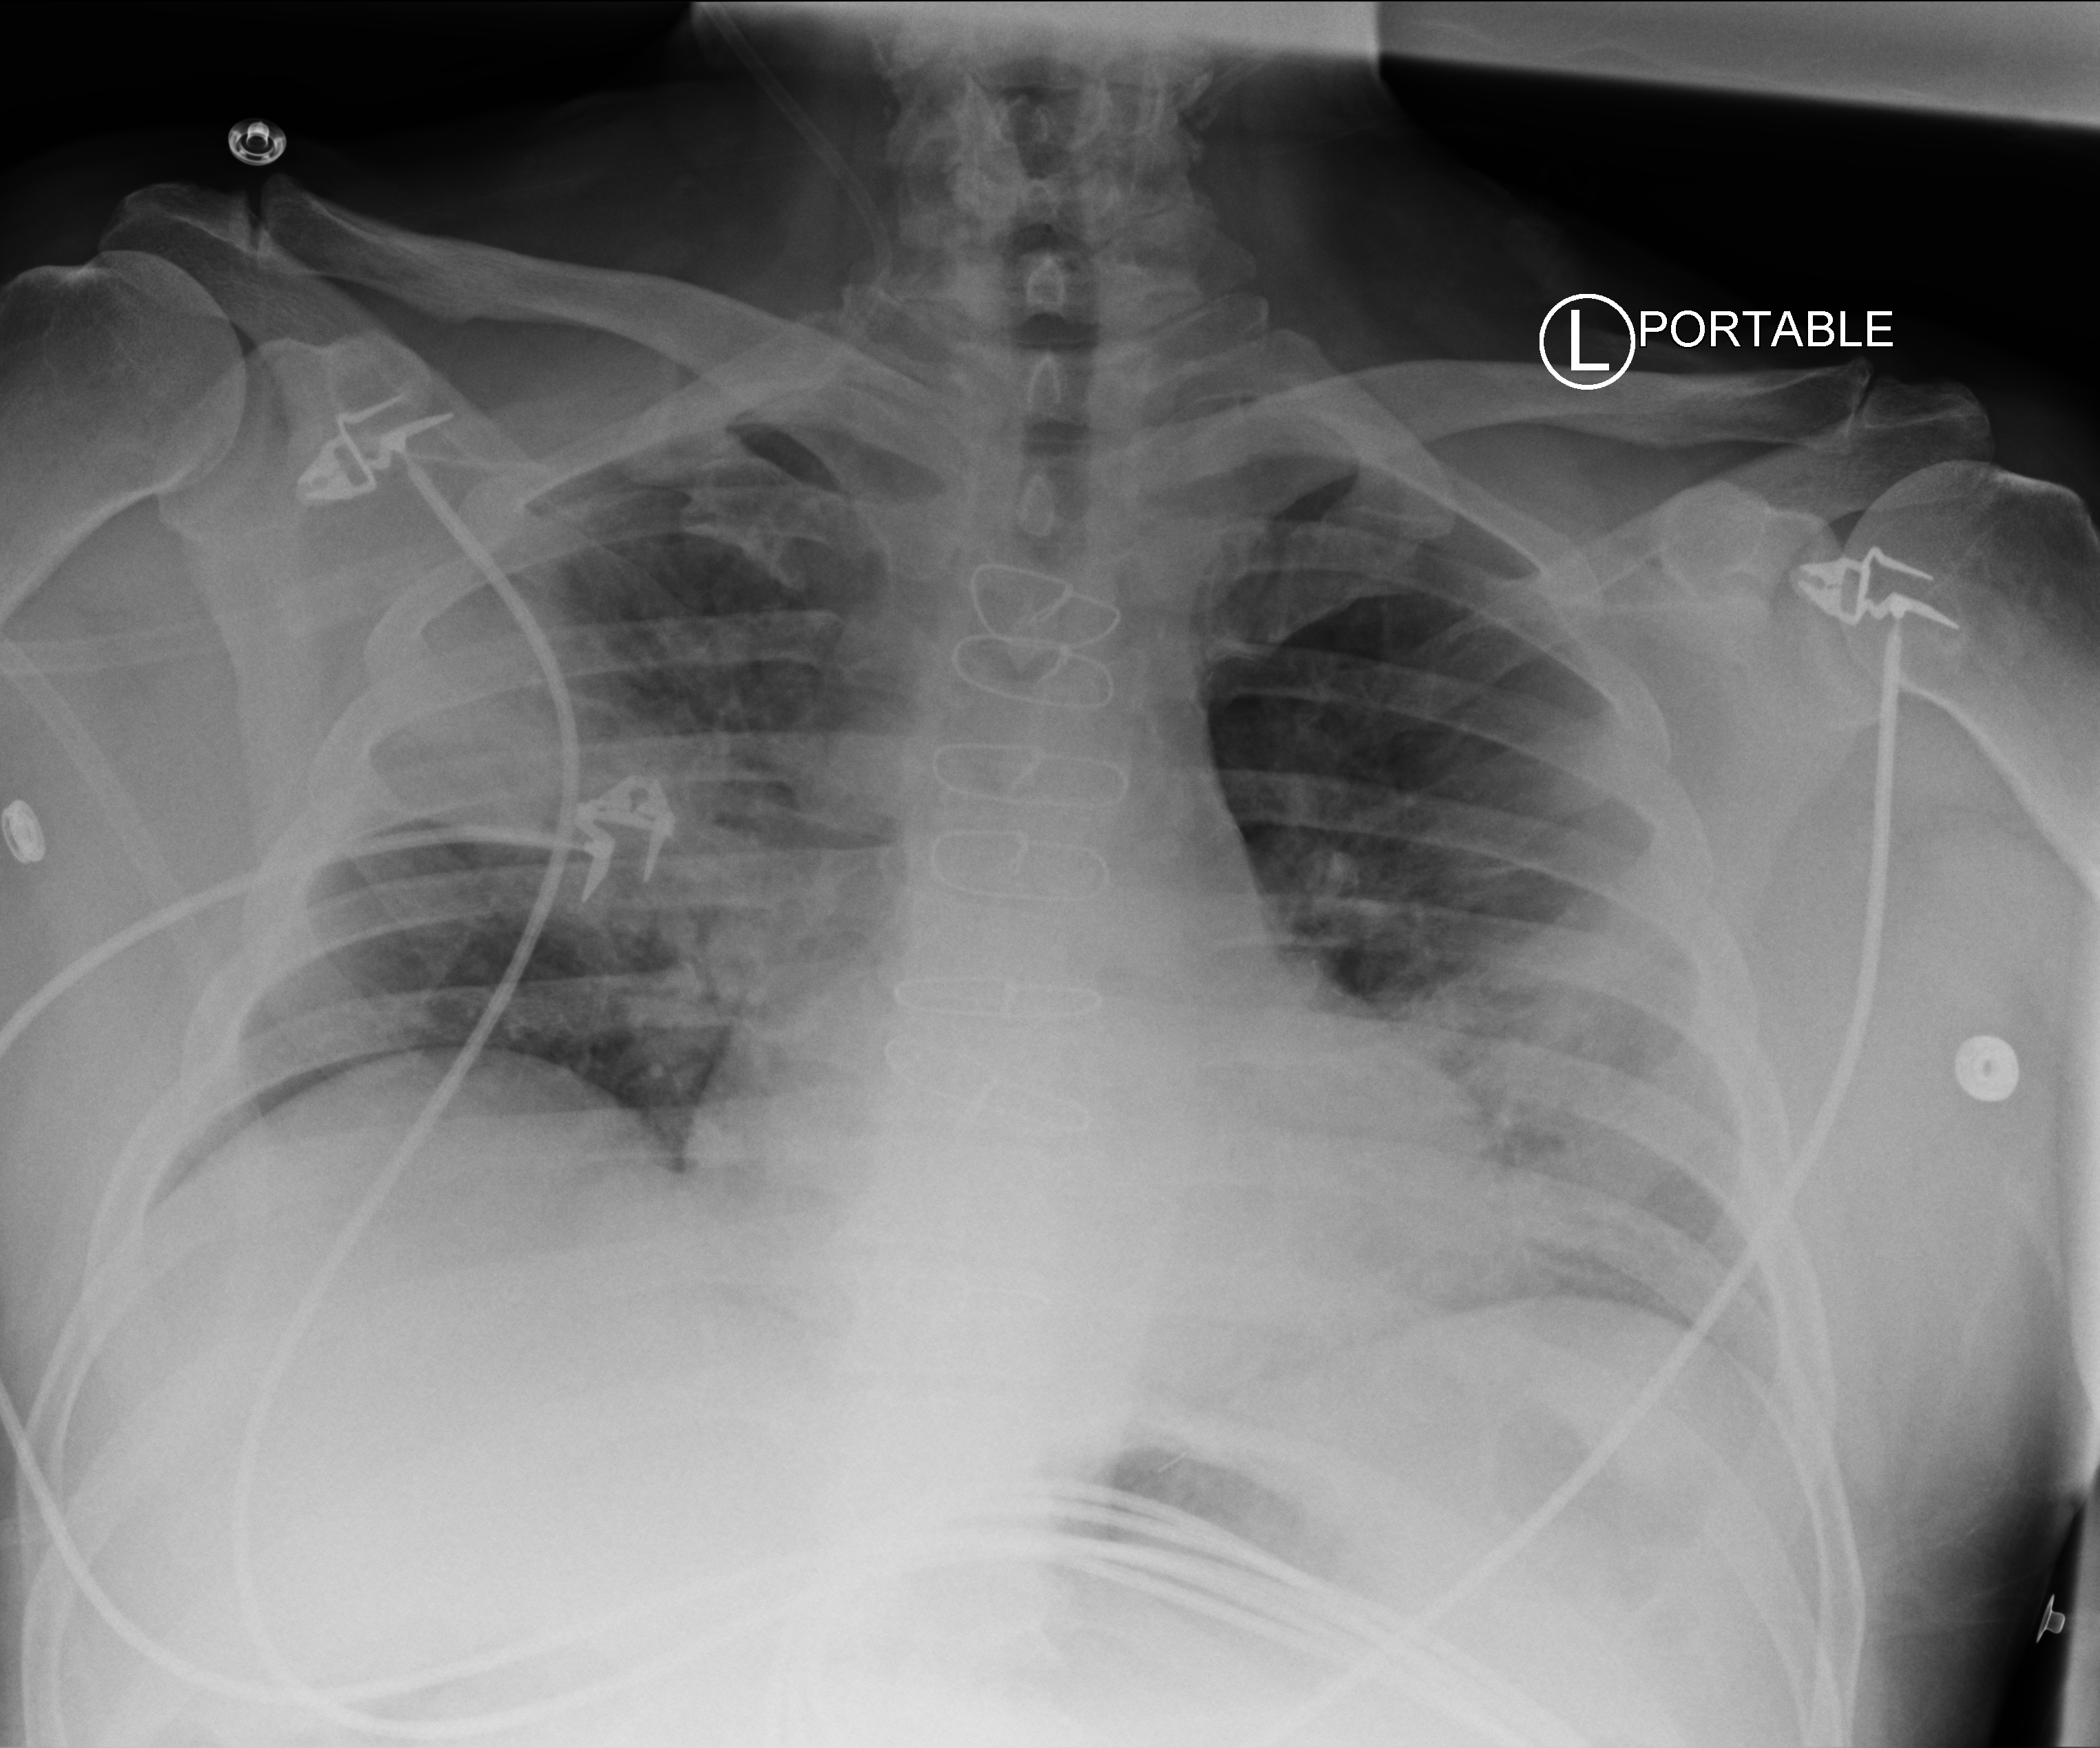
Chest X-ray (portable); anteroposterior (AP) projection. Patient hospitalised with COVID-19; male, aged 60–74 years.
Hospital-stay facts (about this admission, not read from this image; timing relative to this image not recorded): other chronic lung disease (admission record): no; diabetes (admission record): yes.